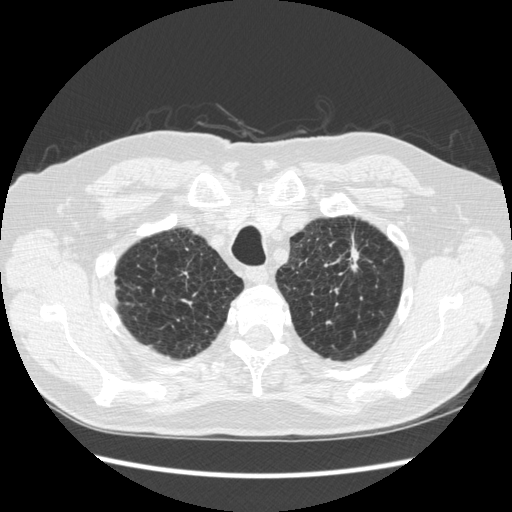
Low-dose screening chest CT, one axial slice. Position 231 of 267 along the scan axis. Lung window (W 1500 / L -600 HU). 512 × 512 image matrix, field of view 360 × 360 mm.
Outlined on this slice (expert manual segmentation):
- lesion 1 (tumor, upper lobe of left lung): box from (x=349, y=247) to (x=359, y=269) px